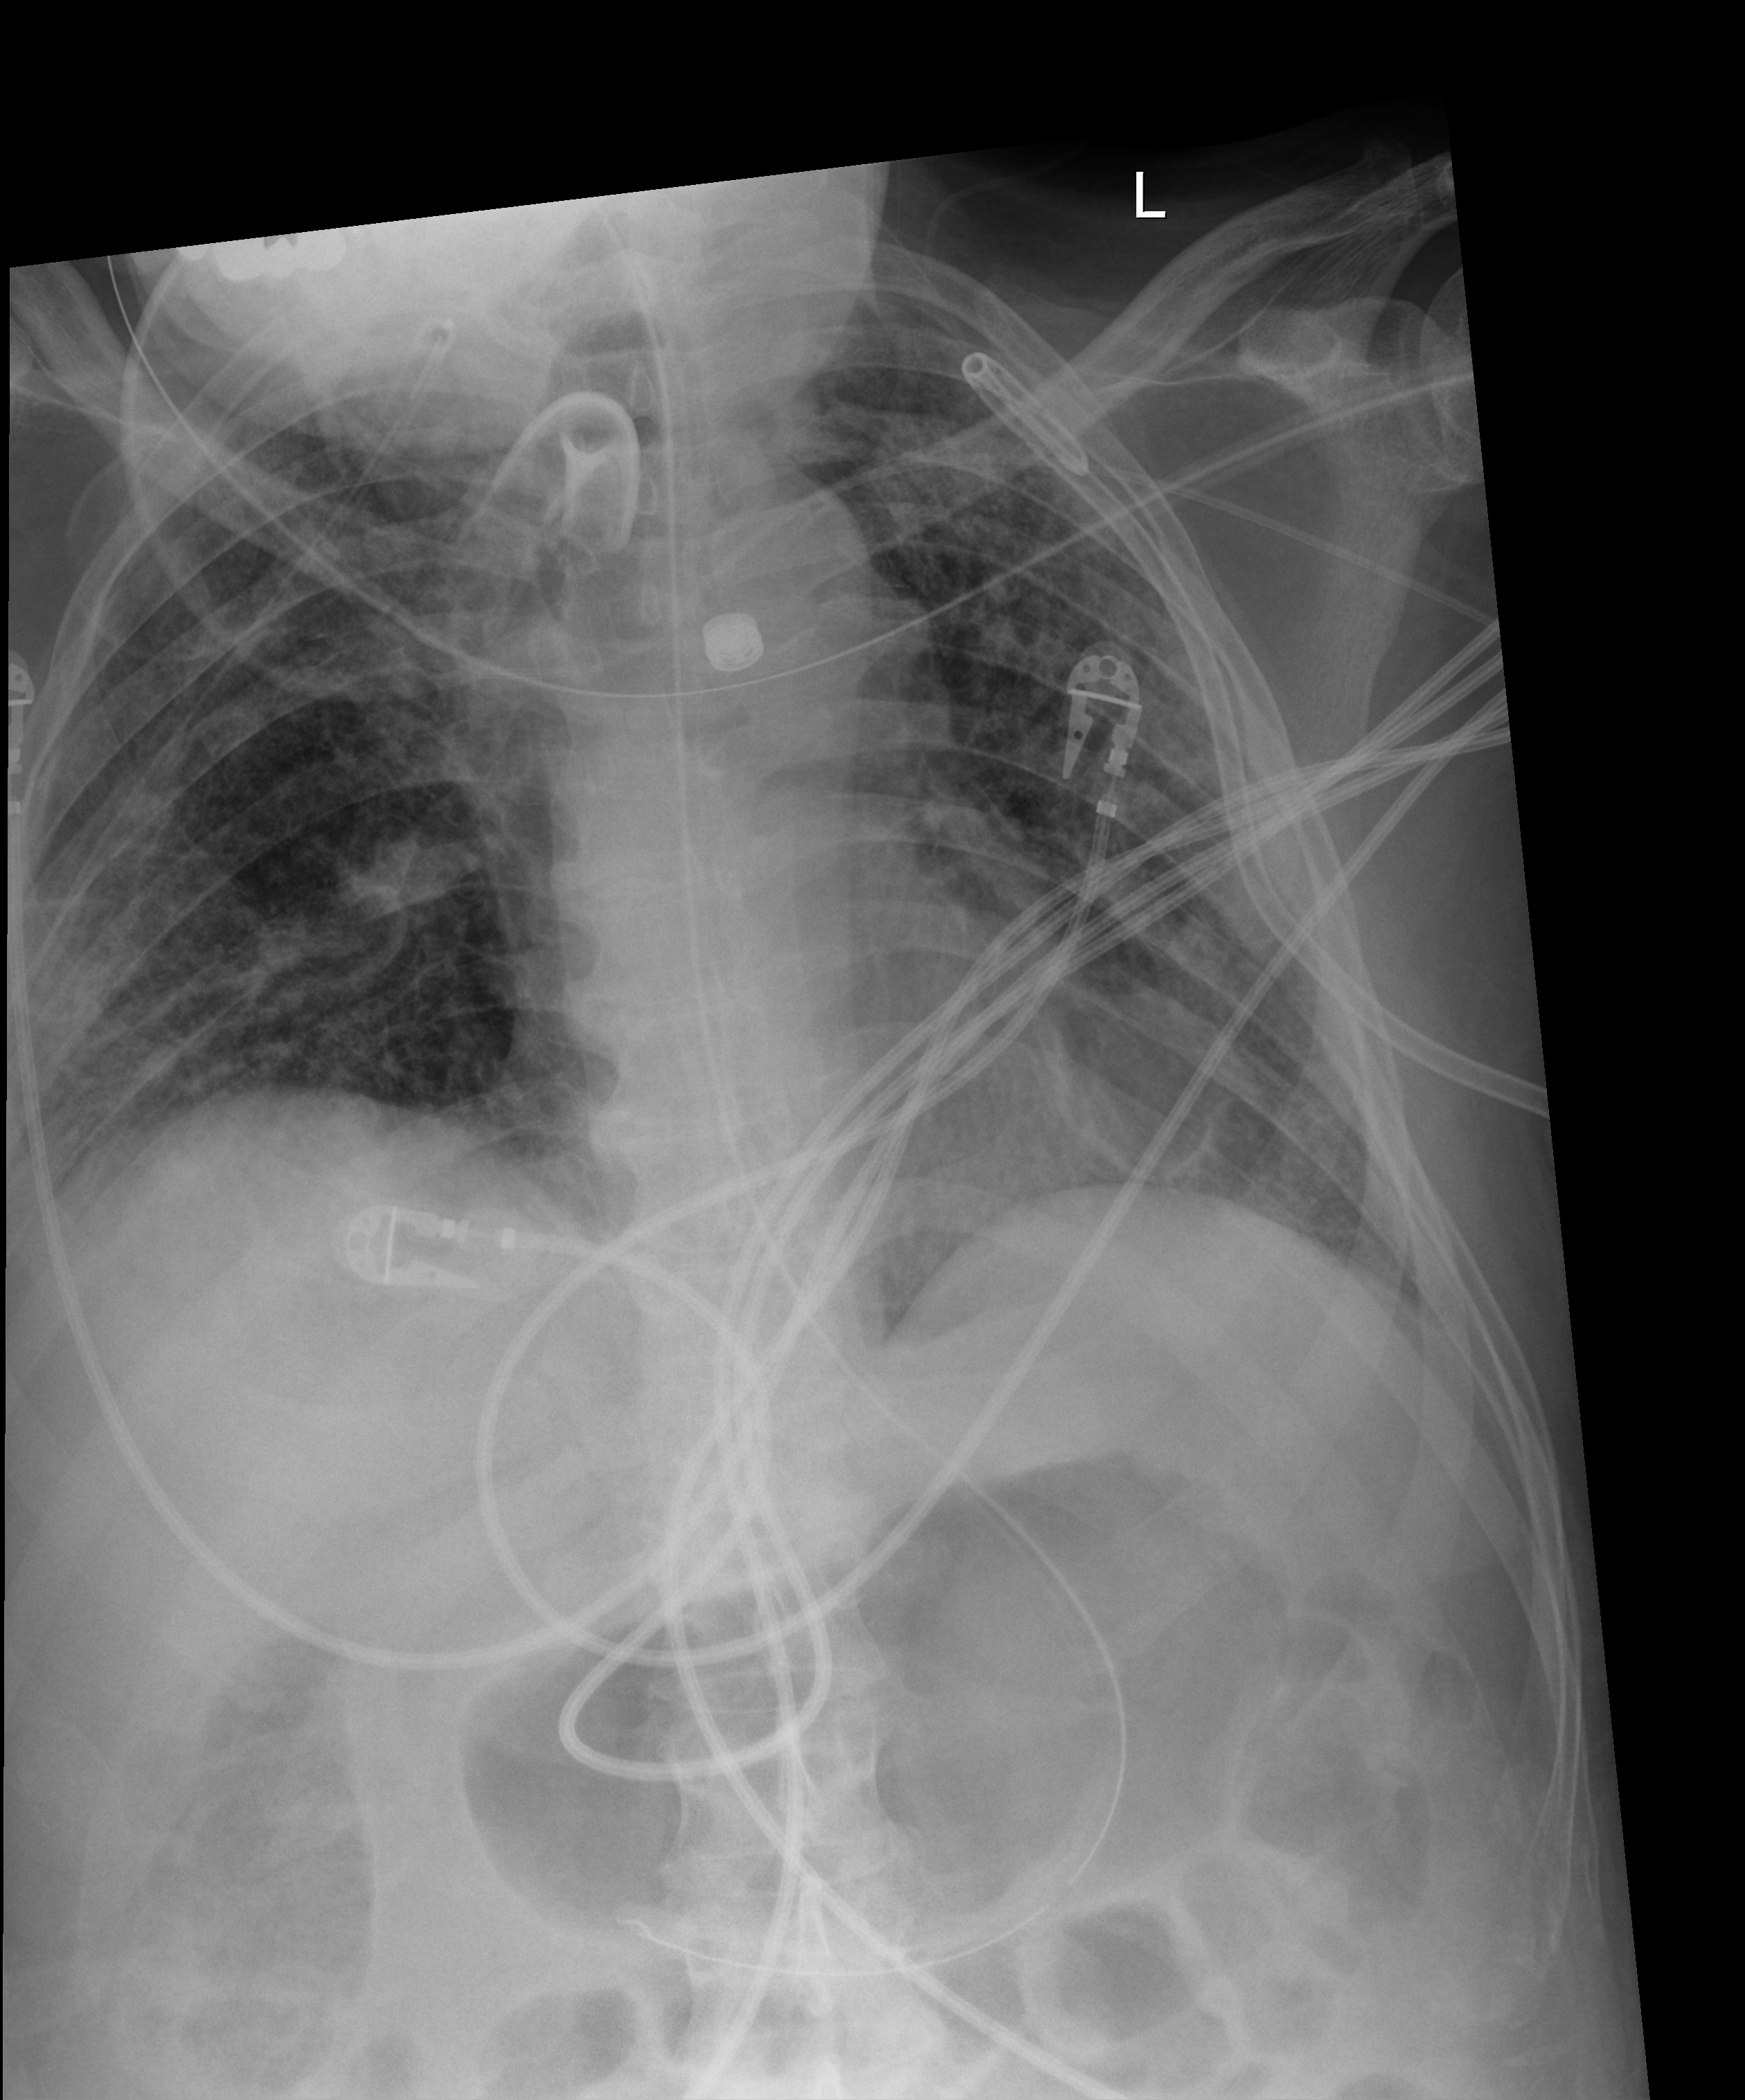
Chest X-ray (portable). Male patient hospitalised with COVID-19, age 18–59 years.
Hospital-stay facts (about this admission, not read from this image; timing relative to this image not recorded): admitted to intensive care during this hospital stay: yes; diabetes (admission record): no; mechanically ventilated during this hospital stay: yes.